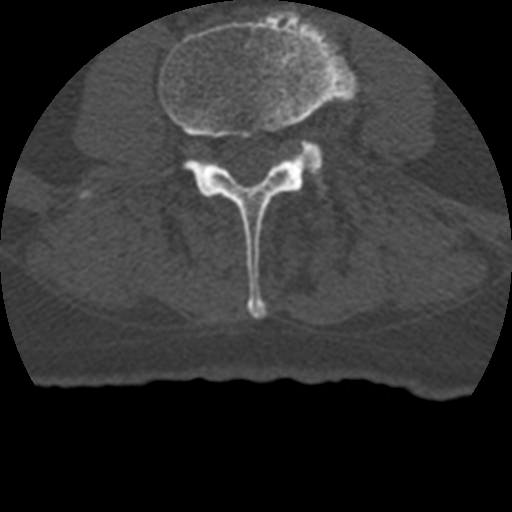
CT including the spine, one axial slice. Slice 86 of 399 in the series (ordered by position). Reconstruction kernel STANDARD. 120 kVp. Bone window (W 1800 / L 400 HU). 1.25 mm slice thickness. 512 × 512 image matrix. Patient age 69 years. From the clinical record (not read from this slice): primary cancer: prostate.
Annotated regions visible in this slice (semi-automatic segmentation, software-assisted and operator-edited):
- L3 vertebra: box from (x=159, y=9) to (x=356, y=319) px
- L4 vertebra: (x=303, y=145)–(x=321, y=170)